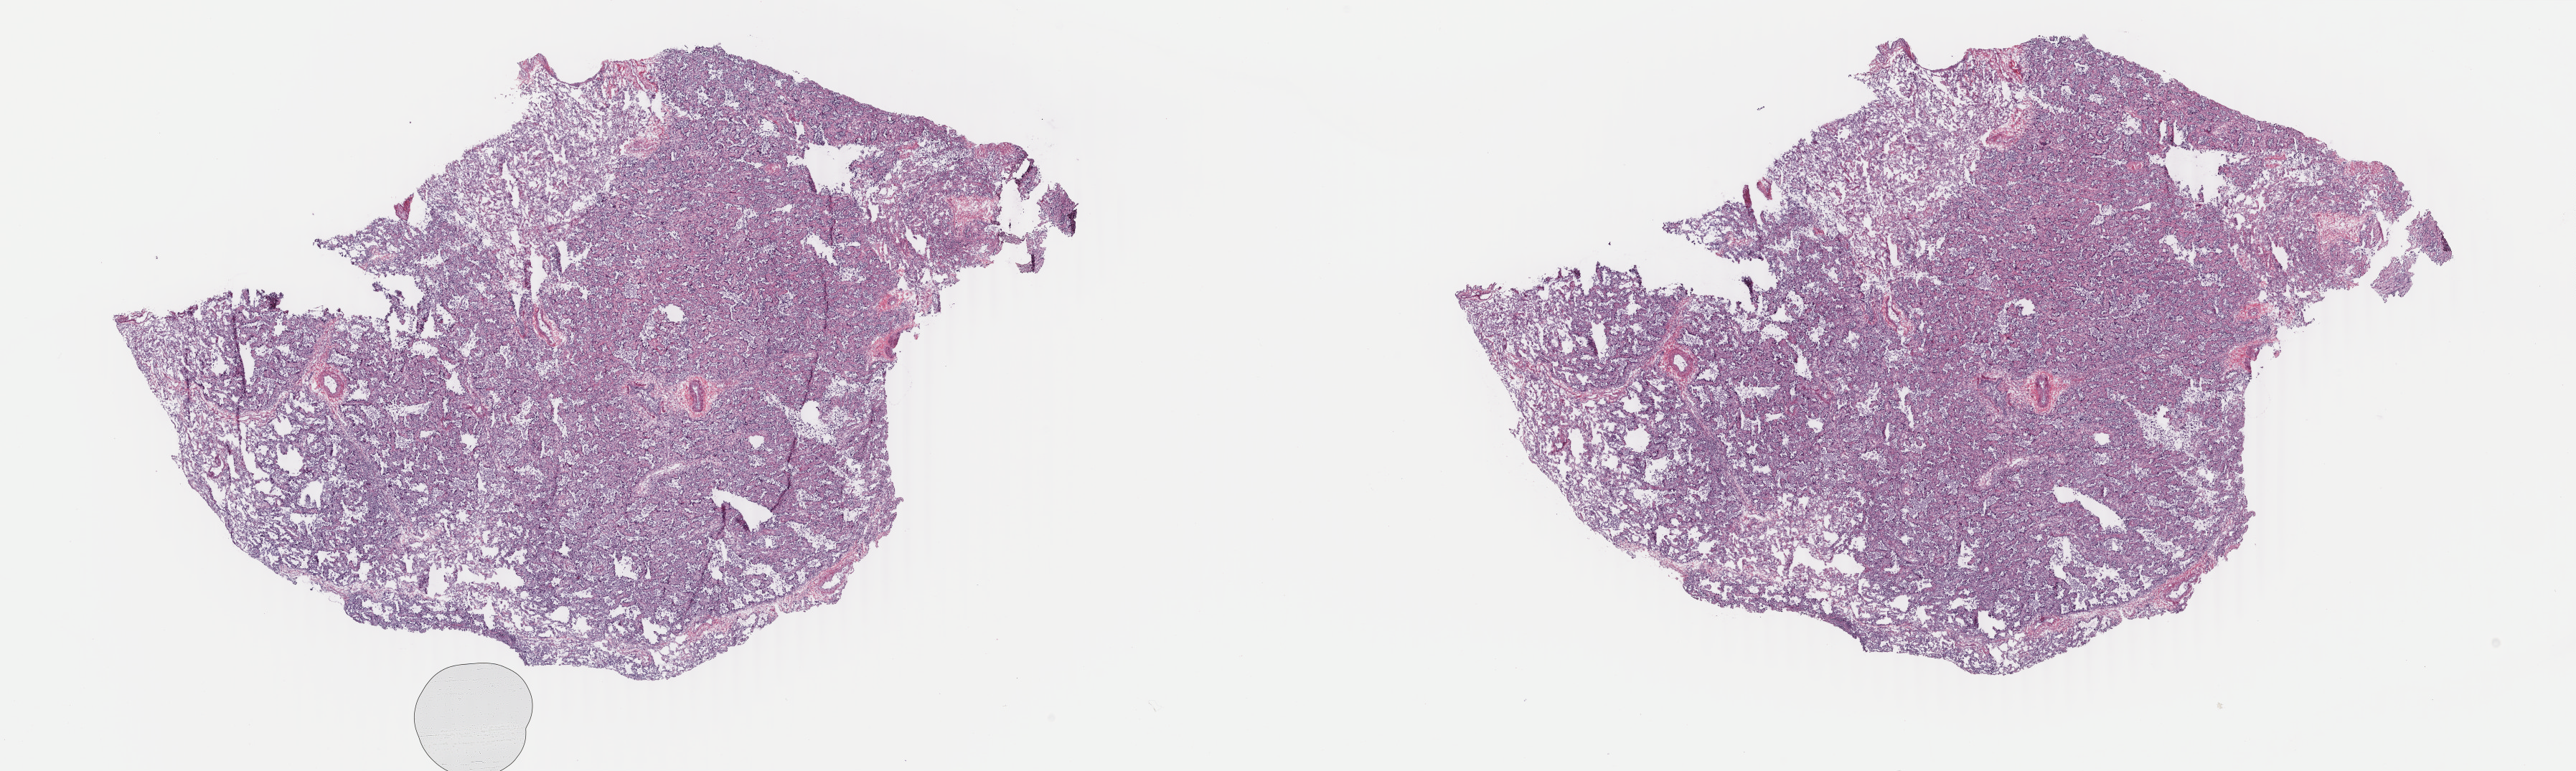
Whole-slide histology image, H&E, whole scanned area (about 28.6 x 8.6 mm) shown as a low-resolution overview. Frozen section. Sample: primary tumour, lung. Female patient; age at initial diagnosis 52 years. Composition of this section per pathologist review: tumour cells 100%, tumour nuclei 65%.
Histologic diagnosis: Adenocarcinoma with mixed subtypes (upper lobe, lung).